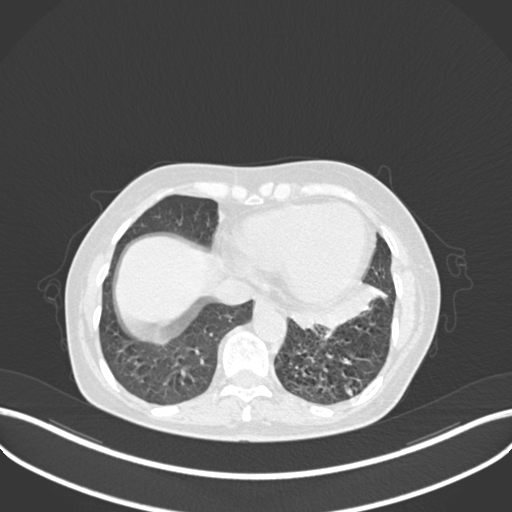
Chest CT, one axial slice; slice 72 of 270 in the series (ordered by position); lung window (W 1500 / L -600 HU); 512 × 512 image matrix. Patient: female, 63 years. Case-level facts recorded for this patient, not image findings: clinical TNM (as recorded): T1b N0 M0.
Outlined on this slice (rectangle marked by the reading radiologist):
- lung tumour (recorded histology: adenocarcinoma): box from (x=282, y=283) to (x=390, y=341) px